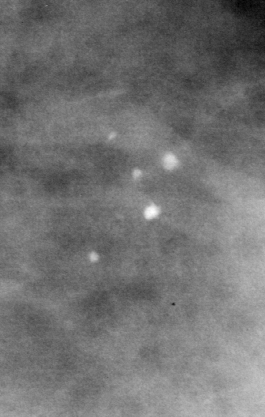
Crop from a digitized film mammogram around one marked abnormality; left breast; MLO view; BI-RADS breast density category 3 (scale 1–4).
Calcifications, morphology pleomorphic, distribution clustered; BI-RADS assessment category 4; subtlety rating 5 on a 1 (subtle) to 5 (obvious) scale; pathology result (as recorded, not read from the image): benign.